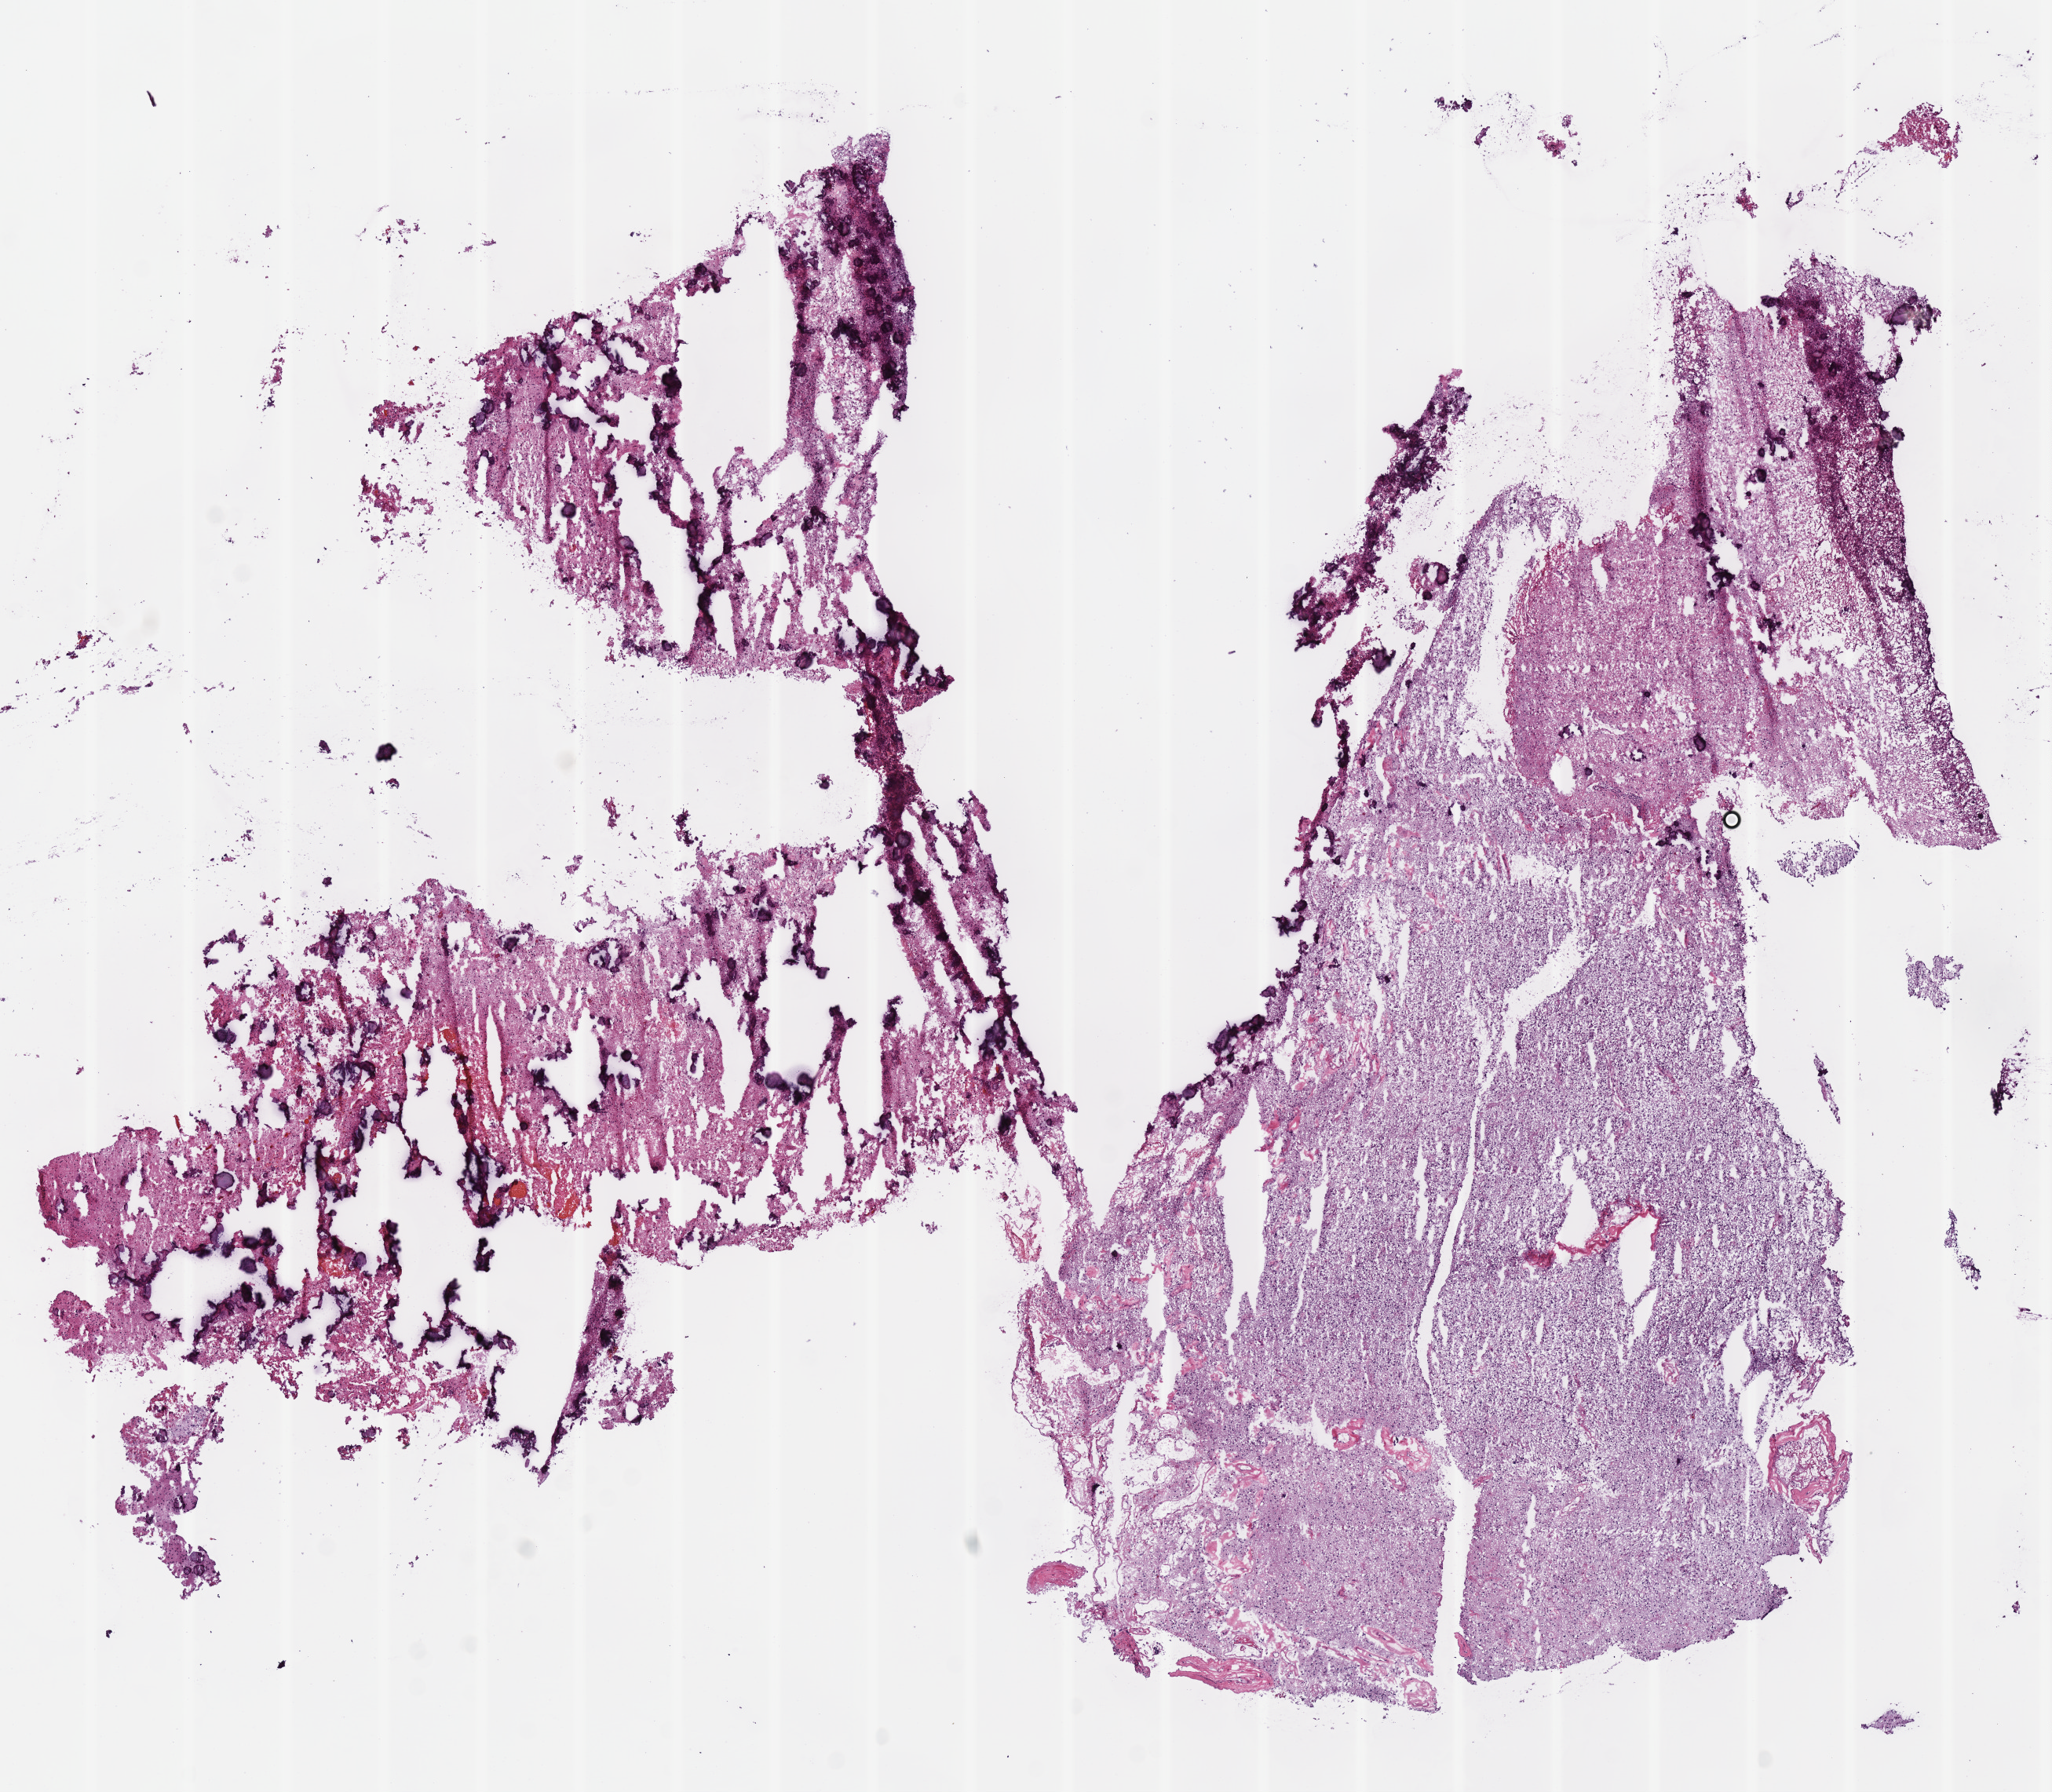
H&E whole-slide image — whole scanned area (about 10.3 x 9.0 mm, from a 40x scan) shown as a low-resolution overview; frozen section from the top of the tissue portion; brain, primary tumour sample. Female, age 31 years at initial diagnosis. Histologic grade: G2 (moderately differentiated). Composition of this section per pathologist review: tumour cells 100%, tumour nuclei 65%, normal cells 0%, stromal cells 0%, necrosis 0%.
• histologic diagnosis: Astrocytoma, NOS (cerebrum)